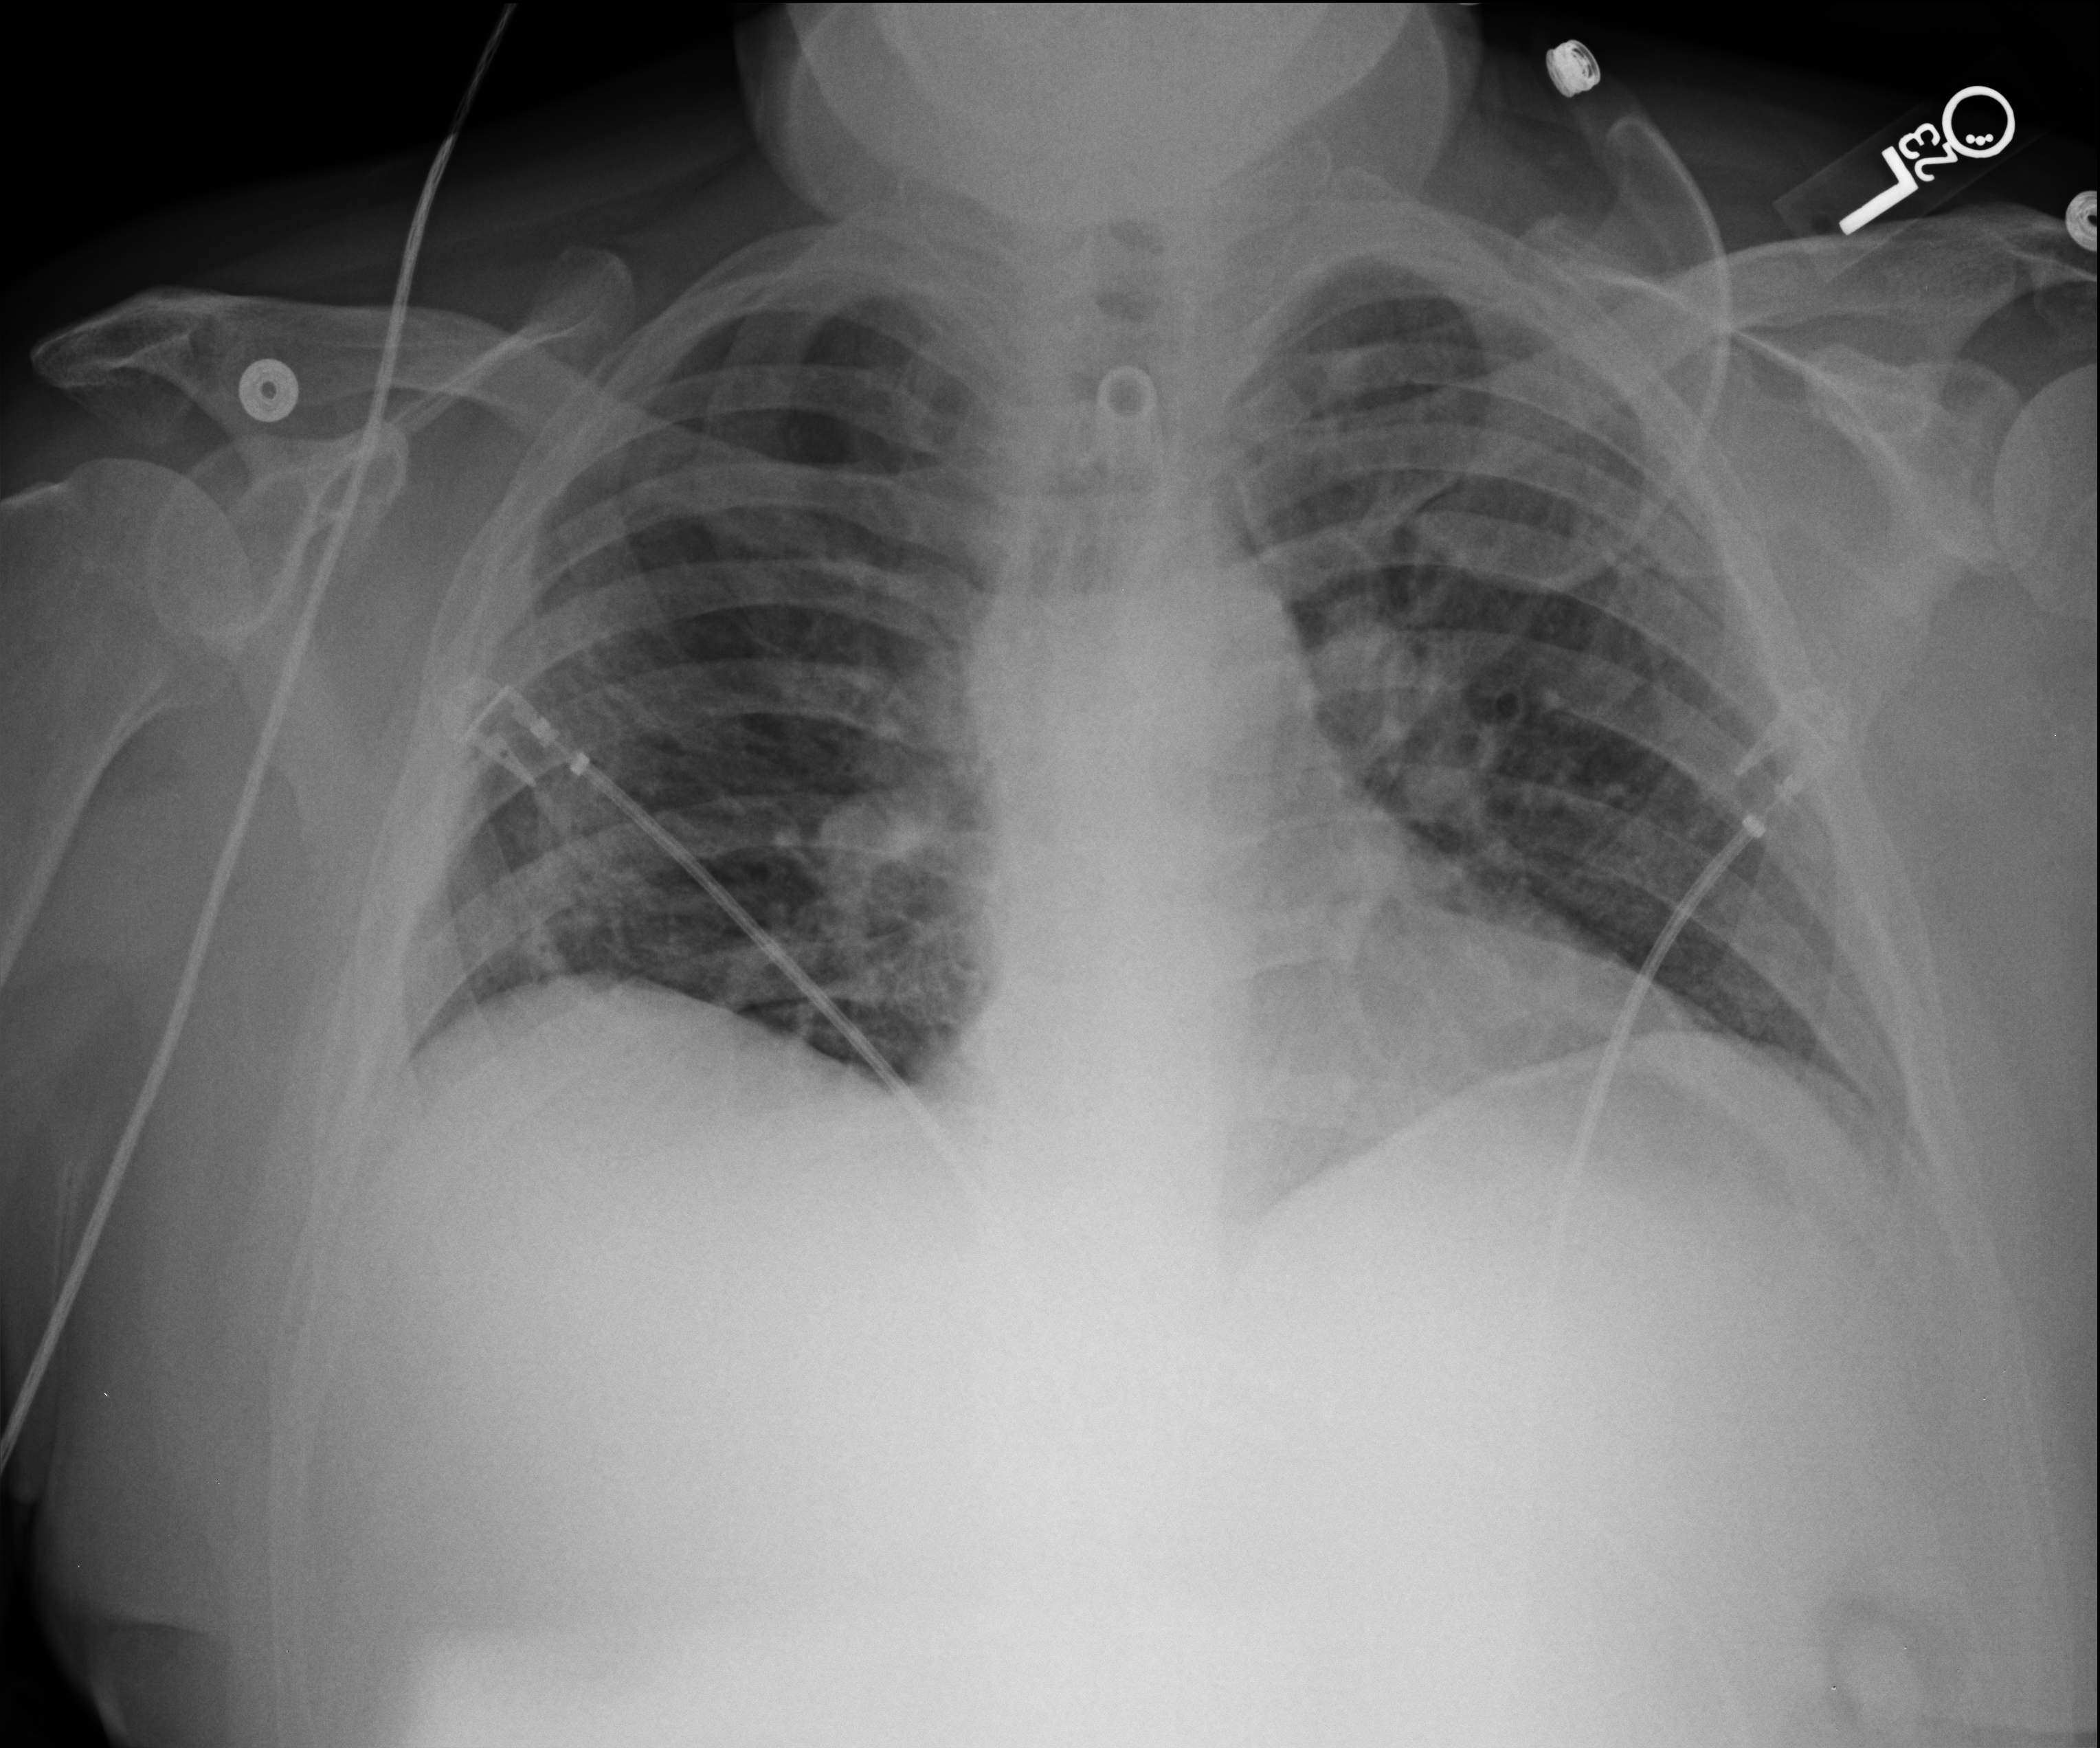
Bedside chest radiograph (computed radiography). Patient hospitalised with COVID-19; male, aged 18–59 years.
From the hospital-stay record, not from the radiograph (when in the stay this image was taken is not recorded): admitted to intensive care during this hospital stay: yes; mechanically ventilated during this hospital stay: yes.